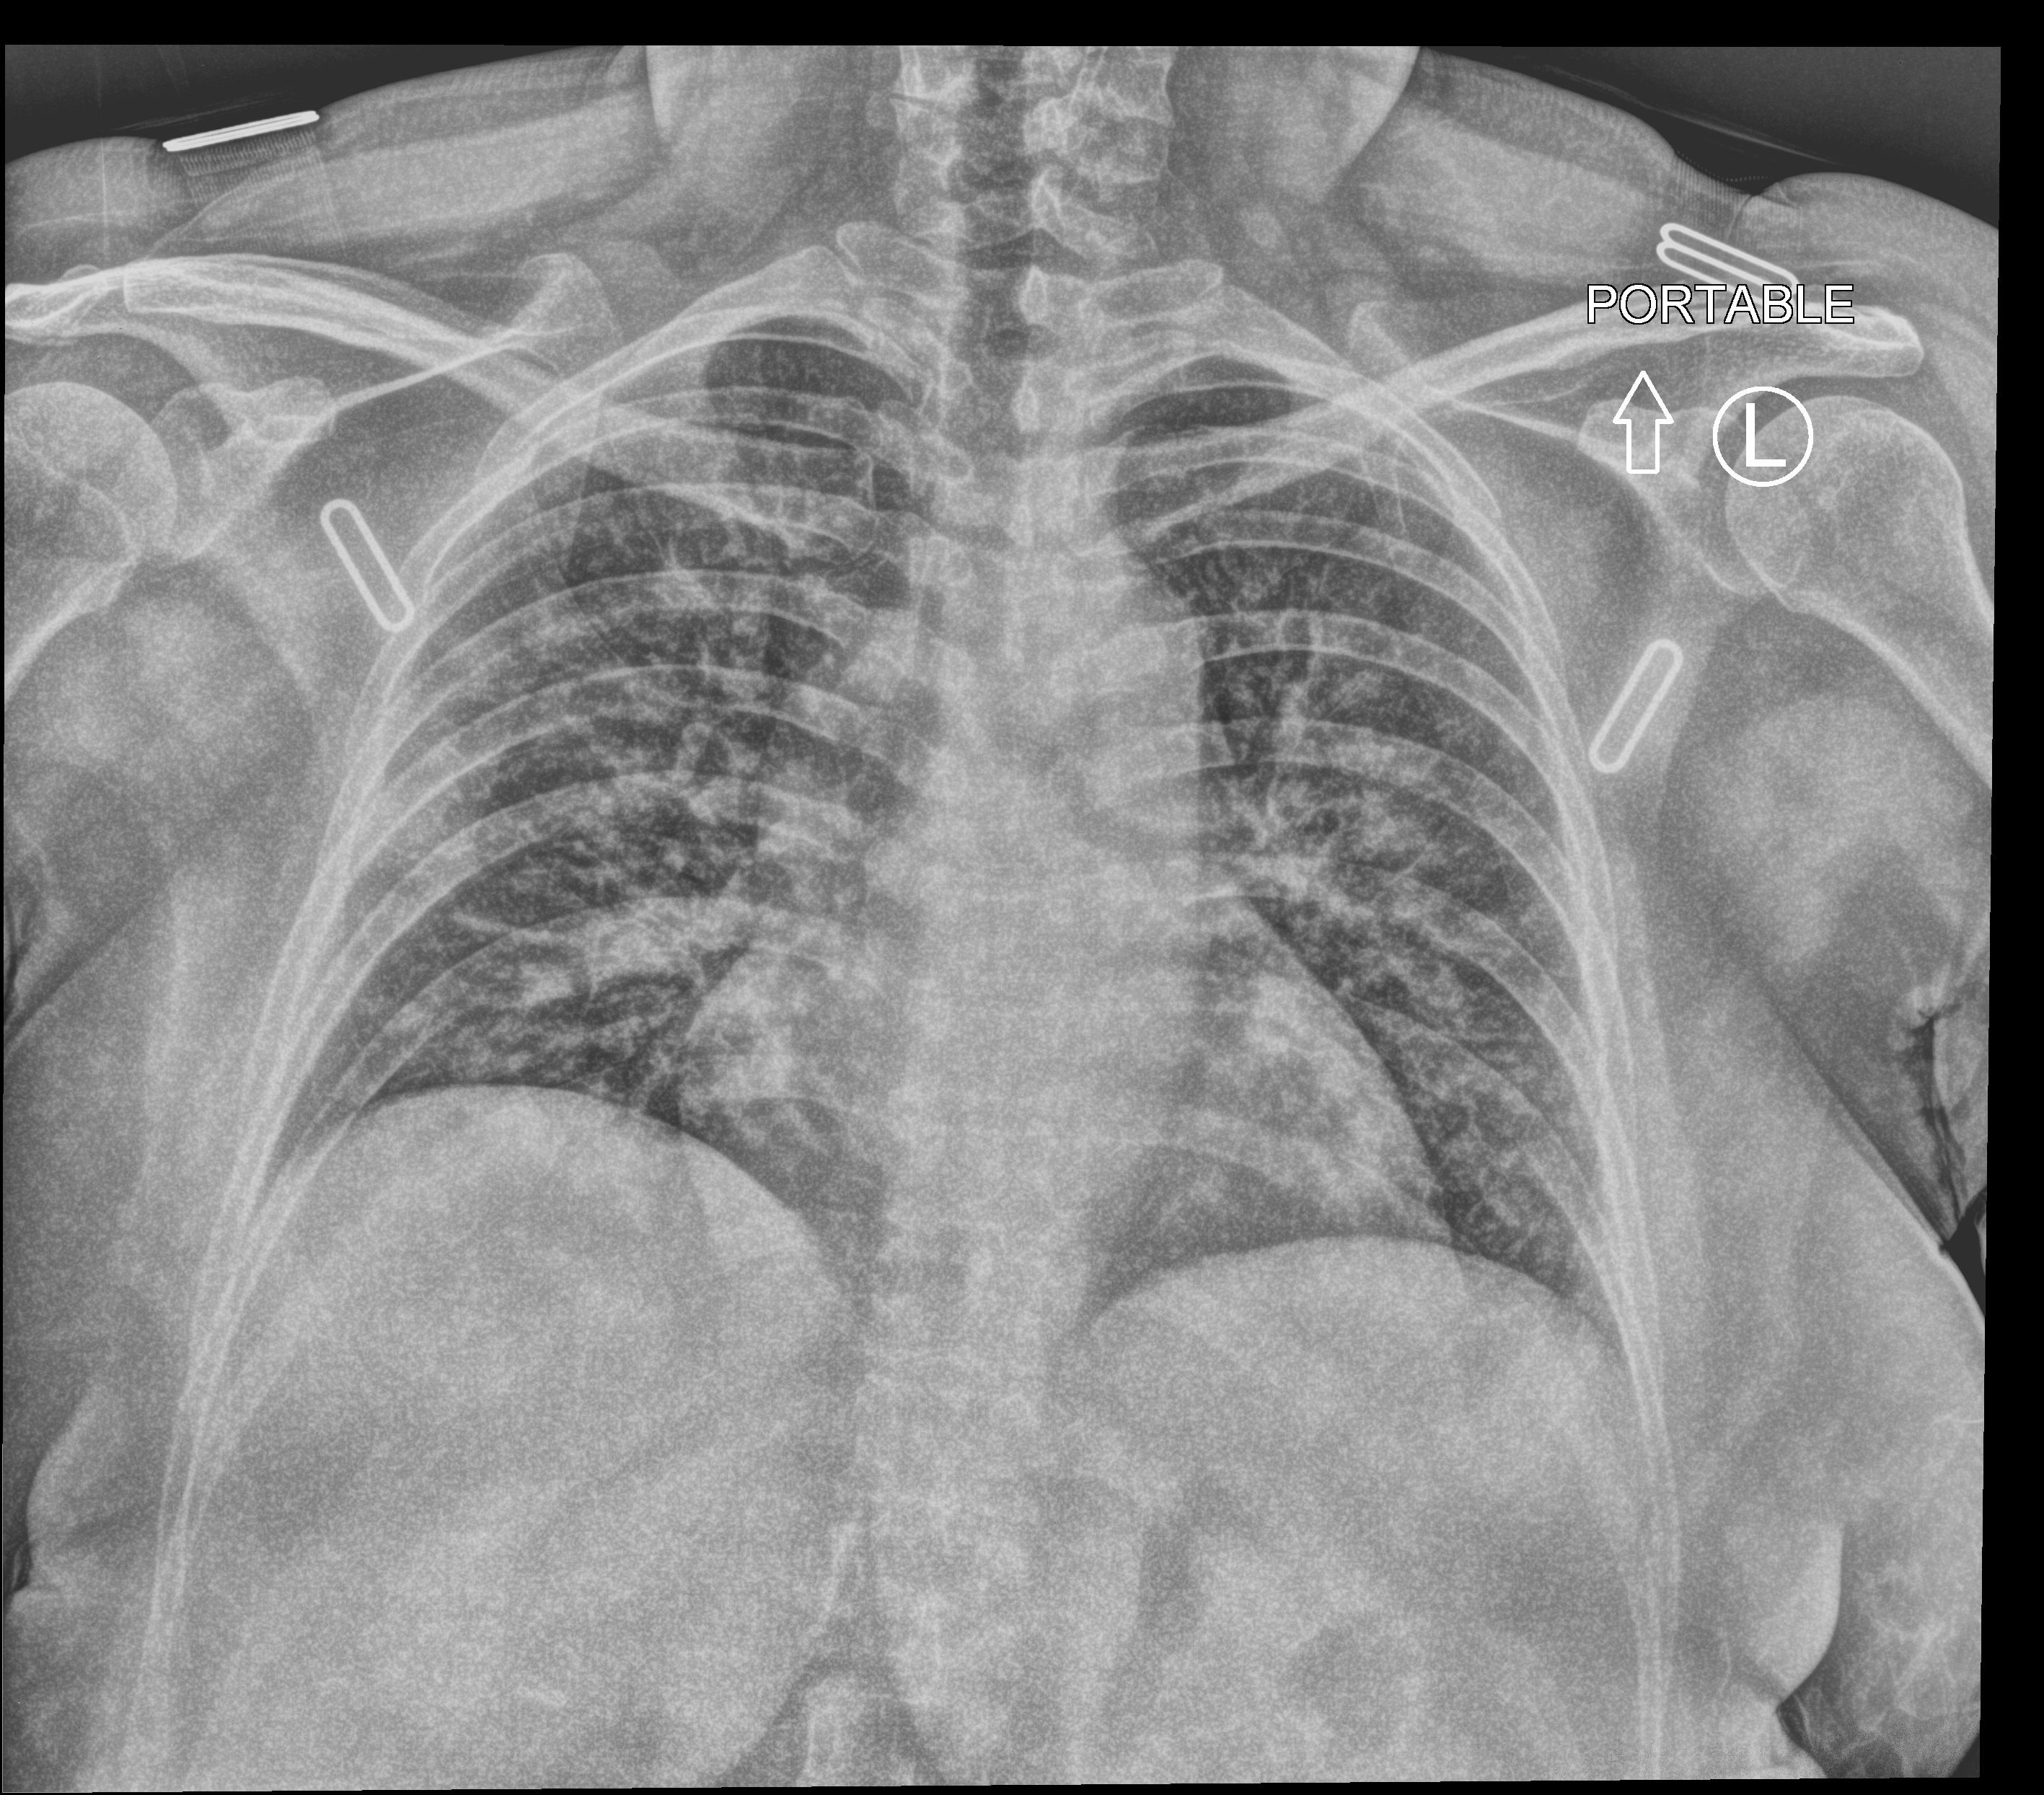
Portable chest radiograph; anteroposterior (AP) projection. Female patient hospitalised with COVID-19, age 18–59 years.
Hospital-stay facts (about this admission, not read from this image; timing relative to this image not recorded): length of hospital stay: 3 days.